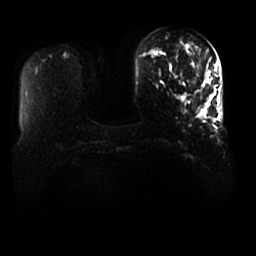
Breast MRI, one axial slice; position 2 of 25 along the scan axis; diffusion-weighted series; image 2 of 4 stored at this slice position (different b-values; order by instance number); 1.5 T; 4 mm slice thickness; 256 × 256 image matrix. Female patient.
Annotated regions visible in this slice (manually delineated by an expert):
- tumour on diffusion-weighted imaging: box from (x=203, y=68) to (x=209, y=80) px